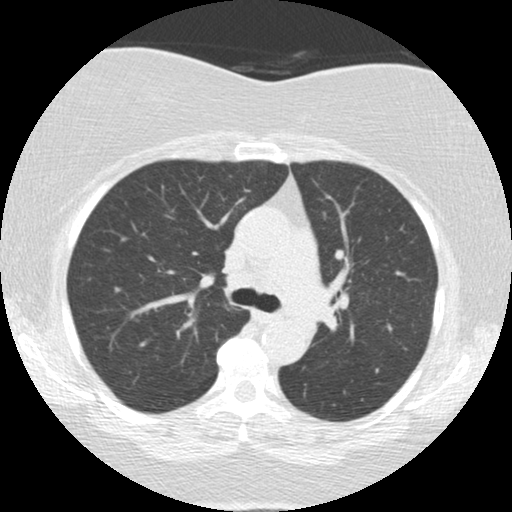
Low-dose screening chest CT, one axial slice; slice 88 of 136 in the series (ordered by position); reconstruction kernel STANDARD; lung window (W 1500 / L -600 HU); 2.5 mm slice thickness; 512 × 512 image matrix.
Annotated regions visible in this slice (manually delineated by an expert):
- lesion 2 (tumor, mediastinum): bounding box <304,284,333,321> (left, top, right, bottom; pixels)